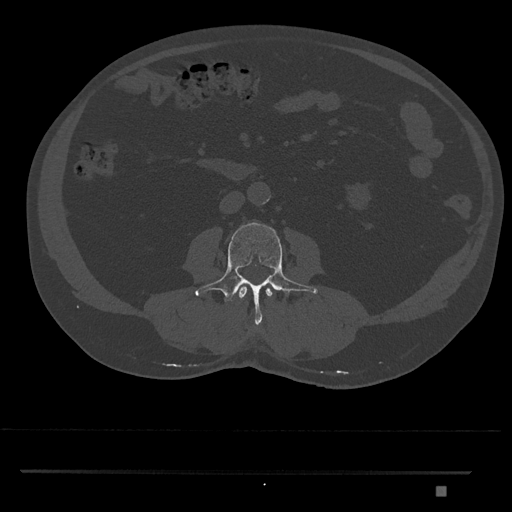
CT including the spine, one axial slice; slice 689 of 1134 in the series (ordered by position); reconstruction kernel Br40s/3; bone window (W 1800 / L 400 HU); 0.5 mm slice thickness; 512 × 512 image matrix, field of view 429 × 429 mm. Male patient, age 65 years. Case-level facts recorded for this patient, not image findings: primary cancer: prostate.
Annotated regions visible in this slice (semi-automatic segmentation, software-assisted and operator-edited):
- L2 vertebra: bounding box [x1, y1, x2, y2] px = [238, 285, 273, 300]
- L3 vertebra: [195, 222, 318, 326]